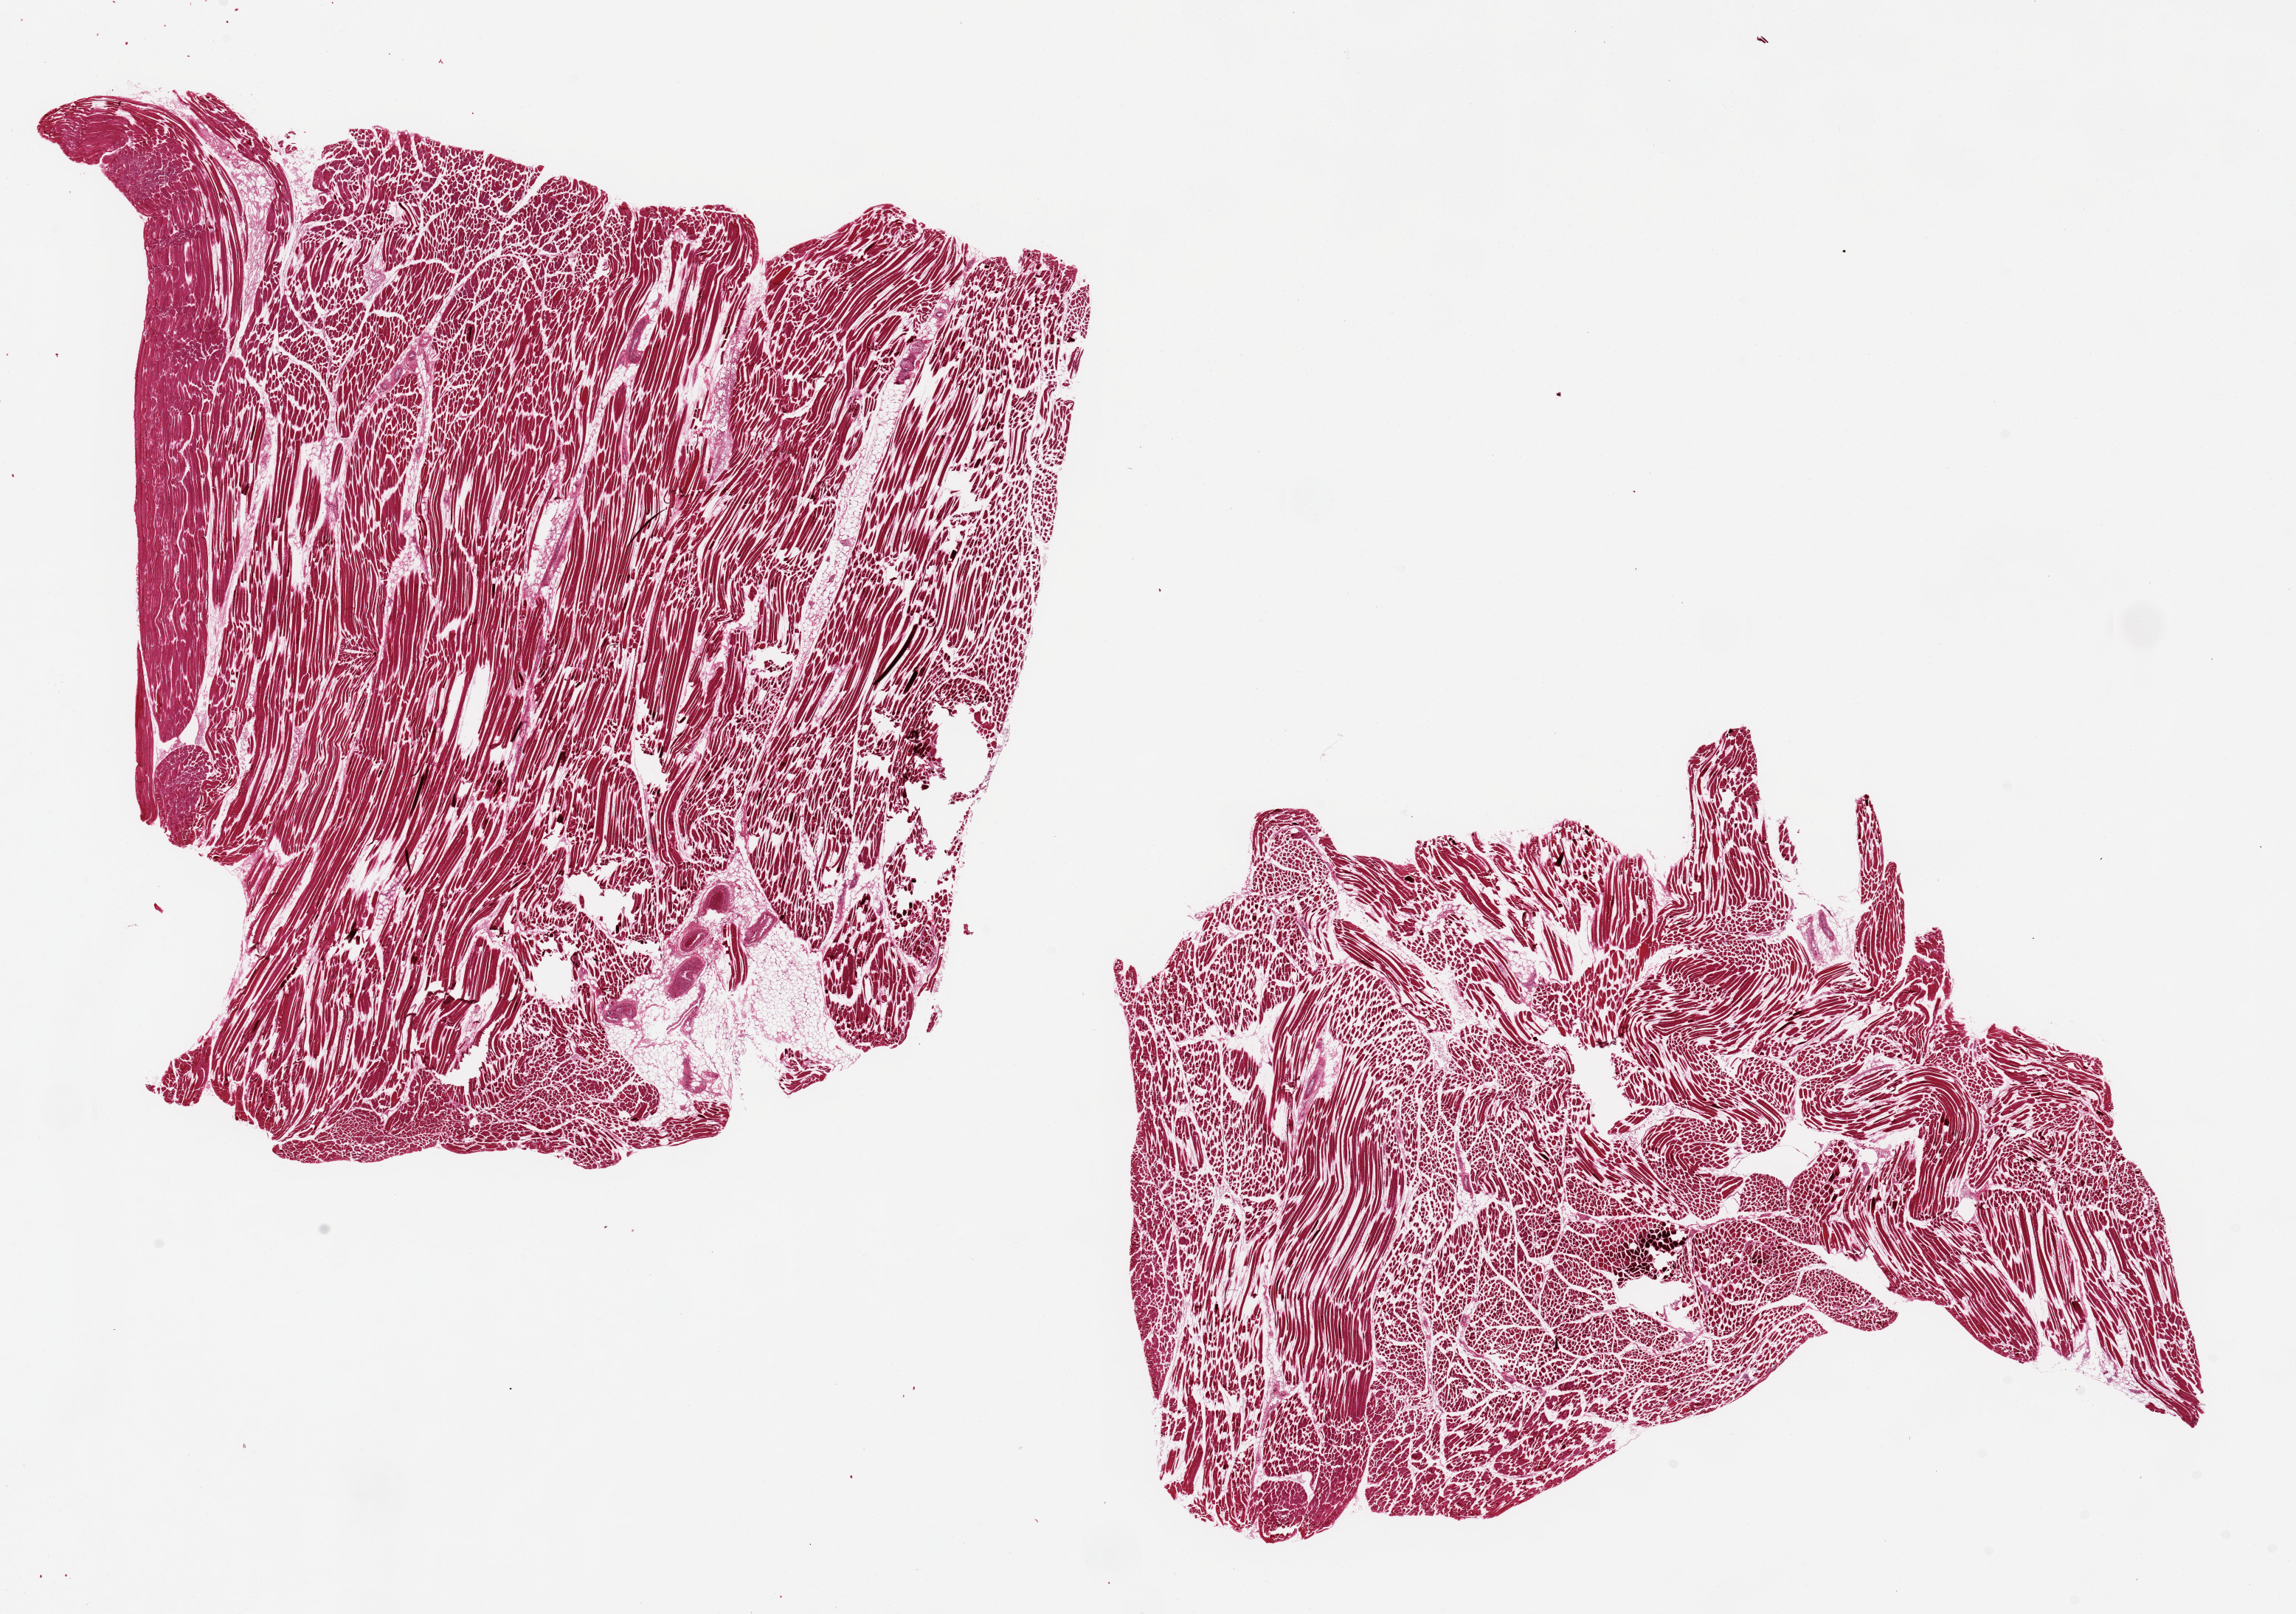
Whole-slide image, haematoxylin and eosin stain, brightfield — low-resolution overview of the scanned area, about 24.6 x 17.3 mm; PAXgene-fixed, paraffin-embedded tissue; sampled site (target tissue): skeletal muscle; donor tissue sample.
Pathologist's review note for this sample: 2 ~ 11x8mm pieces. Interstitial fat <5% of specimens.